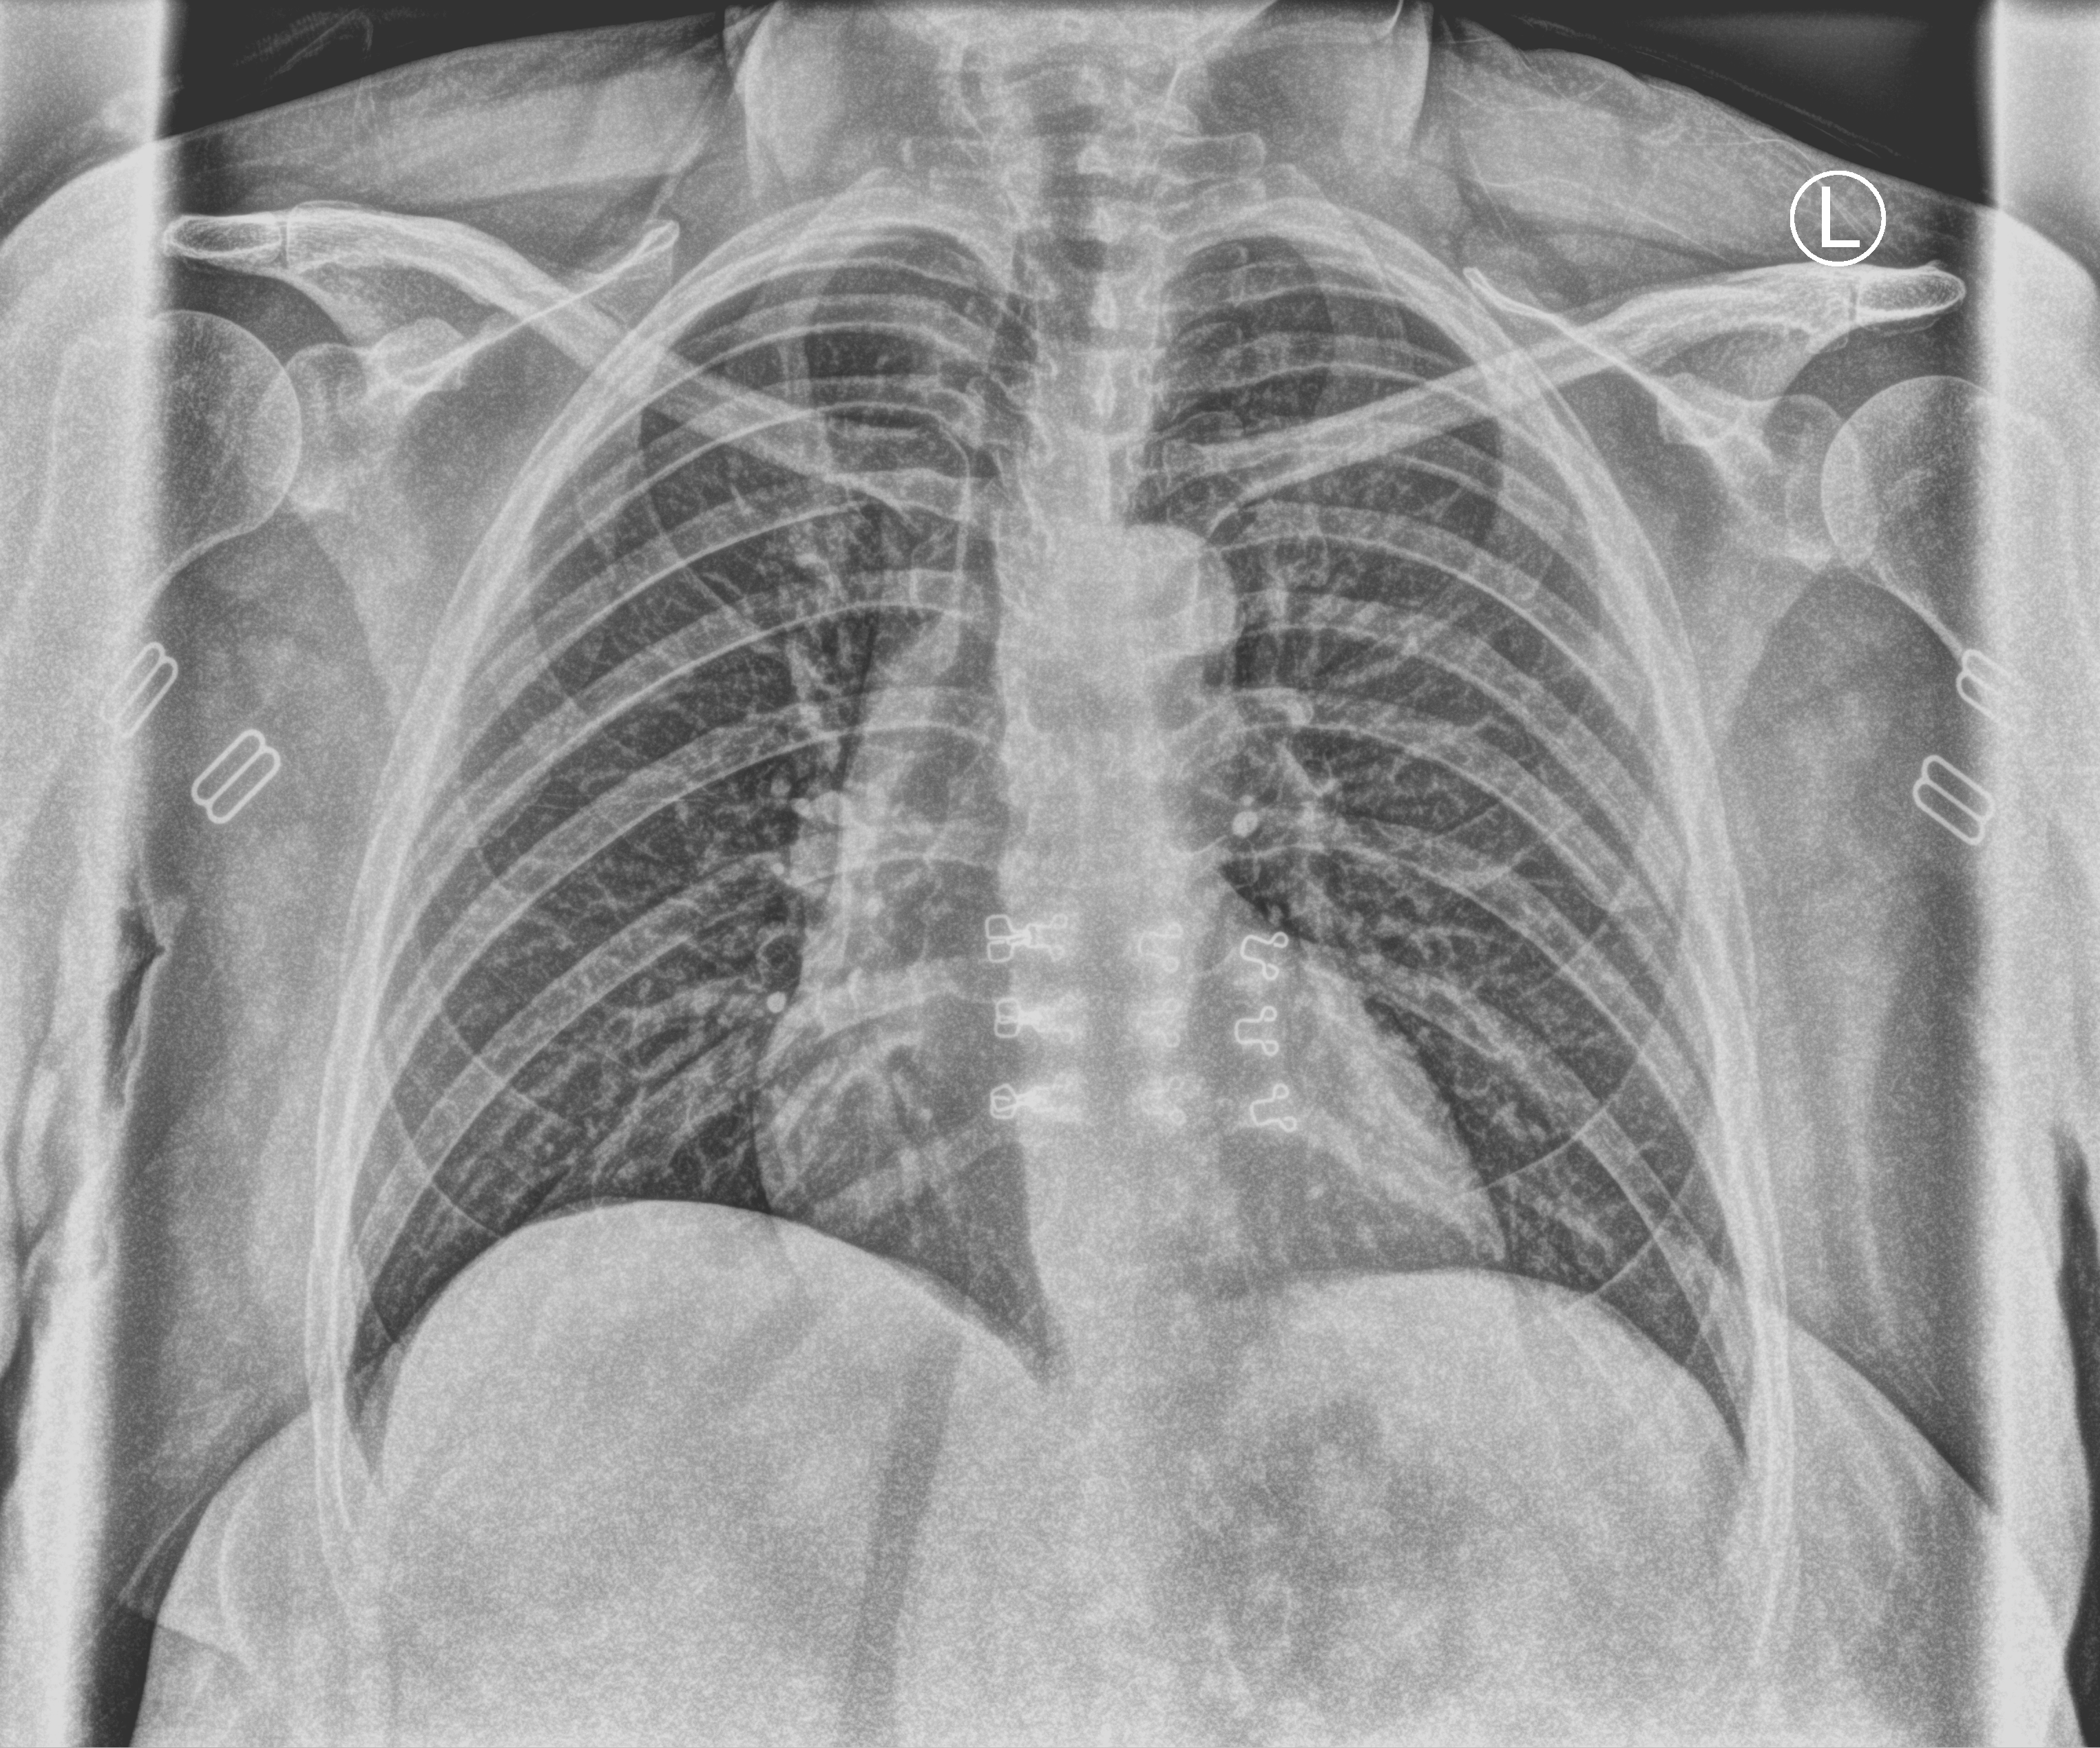
Portable chest radiograph; anteroposterior (AP) projection. Female patient hospitalised with COVID-19, age 18–59 years.
Admission-level facts for this patient (not findings on this image; timing relative to this image not recorded): mechanically ventilated during this hospital stay: no; admitted to intensive care during this hospital stay: no.